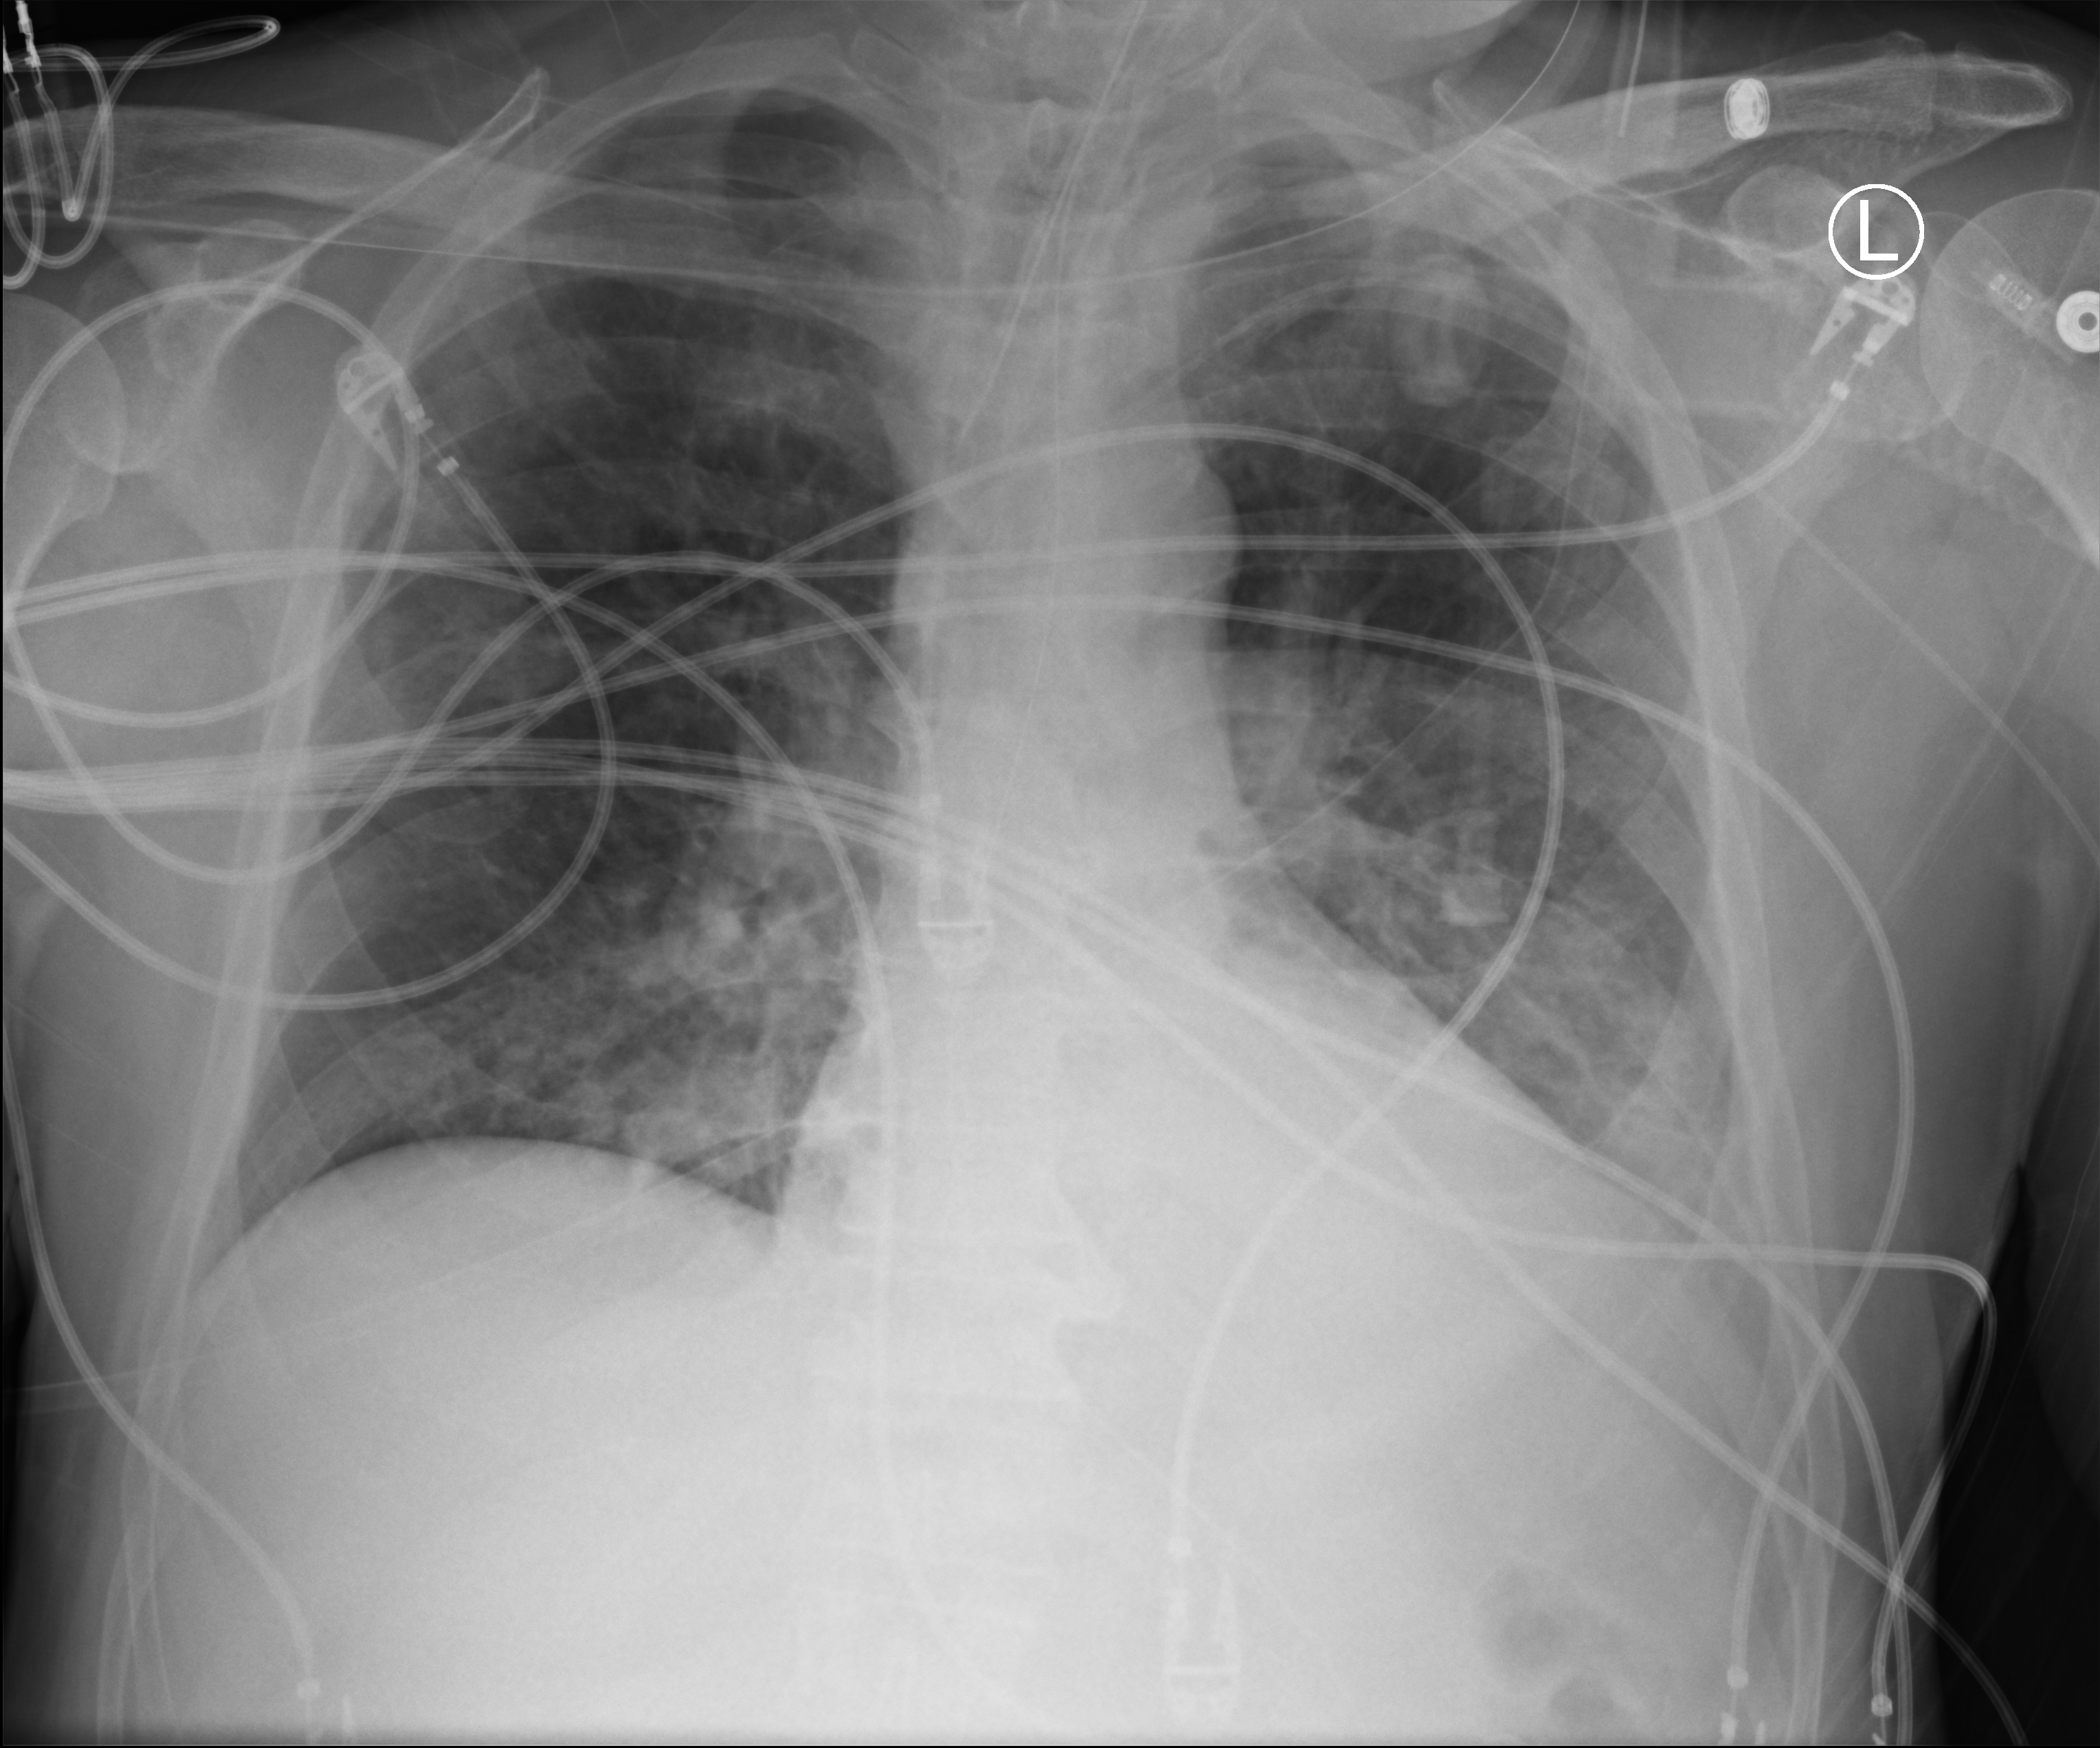
Bedside chest radiograph (computed radiography); anteroposterior (AP) projection. Male patient hospitalised with COVID-19, age 60–74 years.
Hospital-stay facts (about this admission, not read from this image; timing relative to this image not recorded): other chronic lung disease (admission record): no; admitted to intensive care during this hospital stay: yes; length of hospital stay: 35 days.